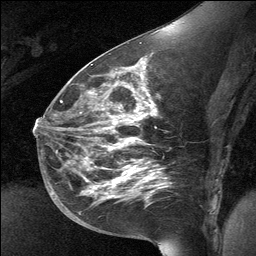
Breast MRI (dynamic contrast-enhanced), one sagittal slice. Dynamic contrast-enhanced study with each time point stored as its own series, time point 2 of 3 at this slice position (early post-contrast, ordered by acquisition time). 1.5 T. TE 4.8 ms, TR 27 ms. 2 mm slice thickness. 256 × 256 image matrix. Female patient, age 39 years. From the clinical record (not read from this slice): setting: breast cancer imaged before/during neoadjuvant chemotherapy; receptor status: HER2-positive.
Annotated regions visible in this slice (semi-automatic segmentation, software-assisted and operator-edited):
- analysis volume of interest (the breast-tissue region the enhancement analysis was run in; not a lesion): bounding box <70,69,163,224> (left, top, right, bottom; pixels)
- tumour enhancement mask (voxels above the 90 % enhancement threshold inside the analysis volume of interest): <94,121,132,188>